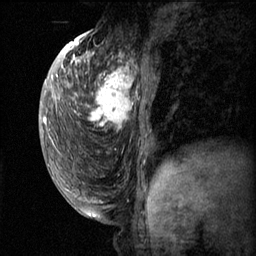
Breast MRI (dynamic contrast-enhanced), one sagittal slice; slice 28 of 60 in the series (ordered by position); dynamic contrast-enhanced series, image 2 of 3 at this slice position (ordered by acquisition); 1.5 T; TE 4.2 ms, TR 11.1 ms; 2 mm slice thickness; 256 × 256 image matrix, field of view 180 × 180 mm. Female patient, age 50 years.
Annotated regions visible in this slice (semi-automatic segmentation, software-assisted and operator-edited):
- analysis volume of interest (the breast-tissue region the enhancement analysis was run in; not a lesion): bounding box [x1, y1, x2, y2] px = [82, 56, 159, 143]
- tumour enhancement mask (voxels above the 70 % enhancement threshold inside the analysis volume of interest): [84, 56, 147, 137]